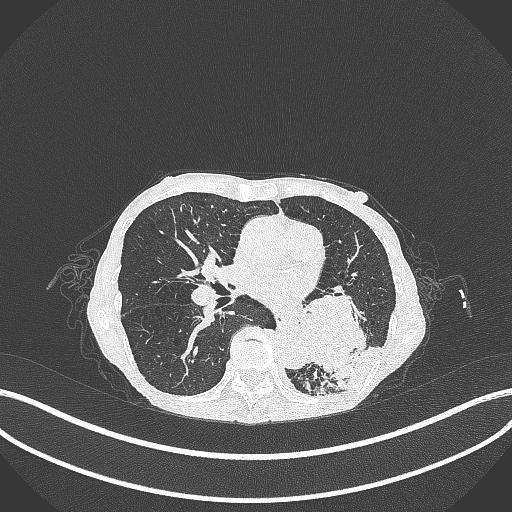
Chest CT, one axial slice. Position 134 of 347 along the scan axis. Reconstruction kernel B70f. Lung window (W 1500 / L -600 HU). 1 mm slice thickness. 512 × 512 image matrix, field of view 400 × 400 mm. Female patient, age 70 years. Case-level facts recorded for this patient, not image findings: clinical TNM (as recorded): T3 N0 M0; histopathological grade: G3.
Structures marked on this image (bounding box drawn by a radiologist):
- lung tumour (recorded histology: small cell carcinoma): box from (x=298, y=281) to (x=377, y=378) px